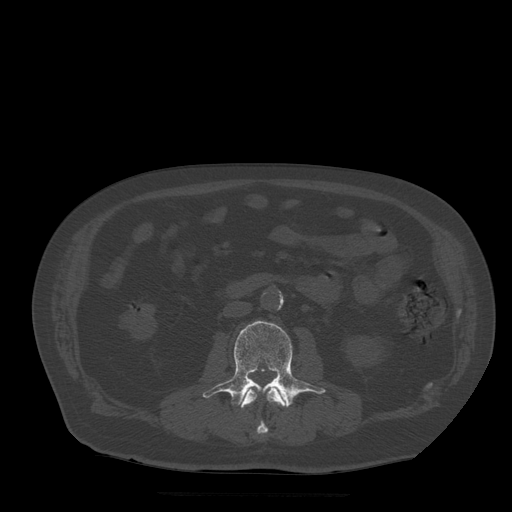
CT including the spine, one axial slice; position 146 of 522 along the scan axis; bone window (W 1800 / L 400 HU); 512 × 512 image matrix, field of view 420 × 420 mm. Patient age 72 years. Case-level facts recorded for this patient, not image findings: primary cancer: prostate.
Outlined on this slice (semi-automatically segmented with operator editing):
- L2 vertebra: bounding box [x1, y1, x2, y2] px = [240, 383, 288, 436]
- L3 vertebra: [203, 321, 326, 407]